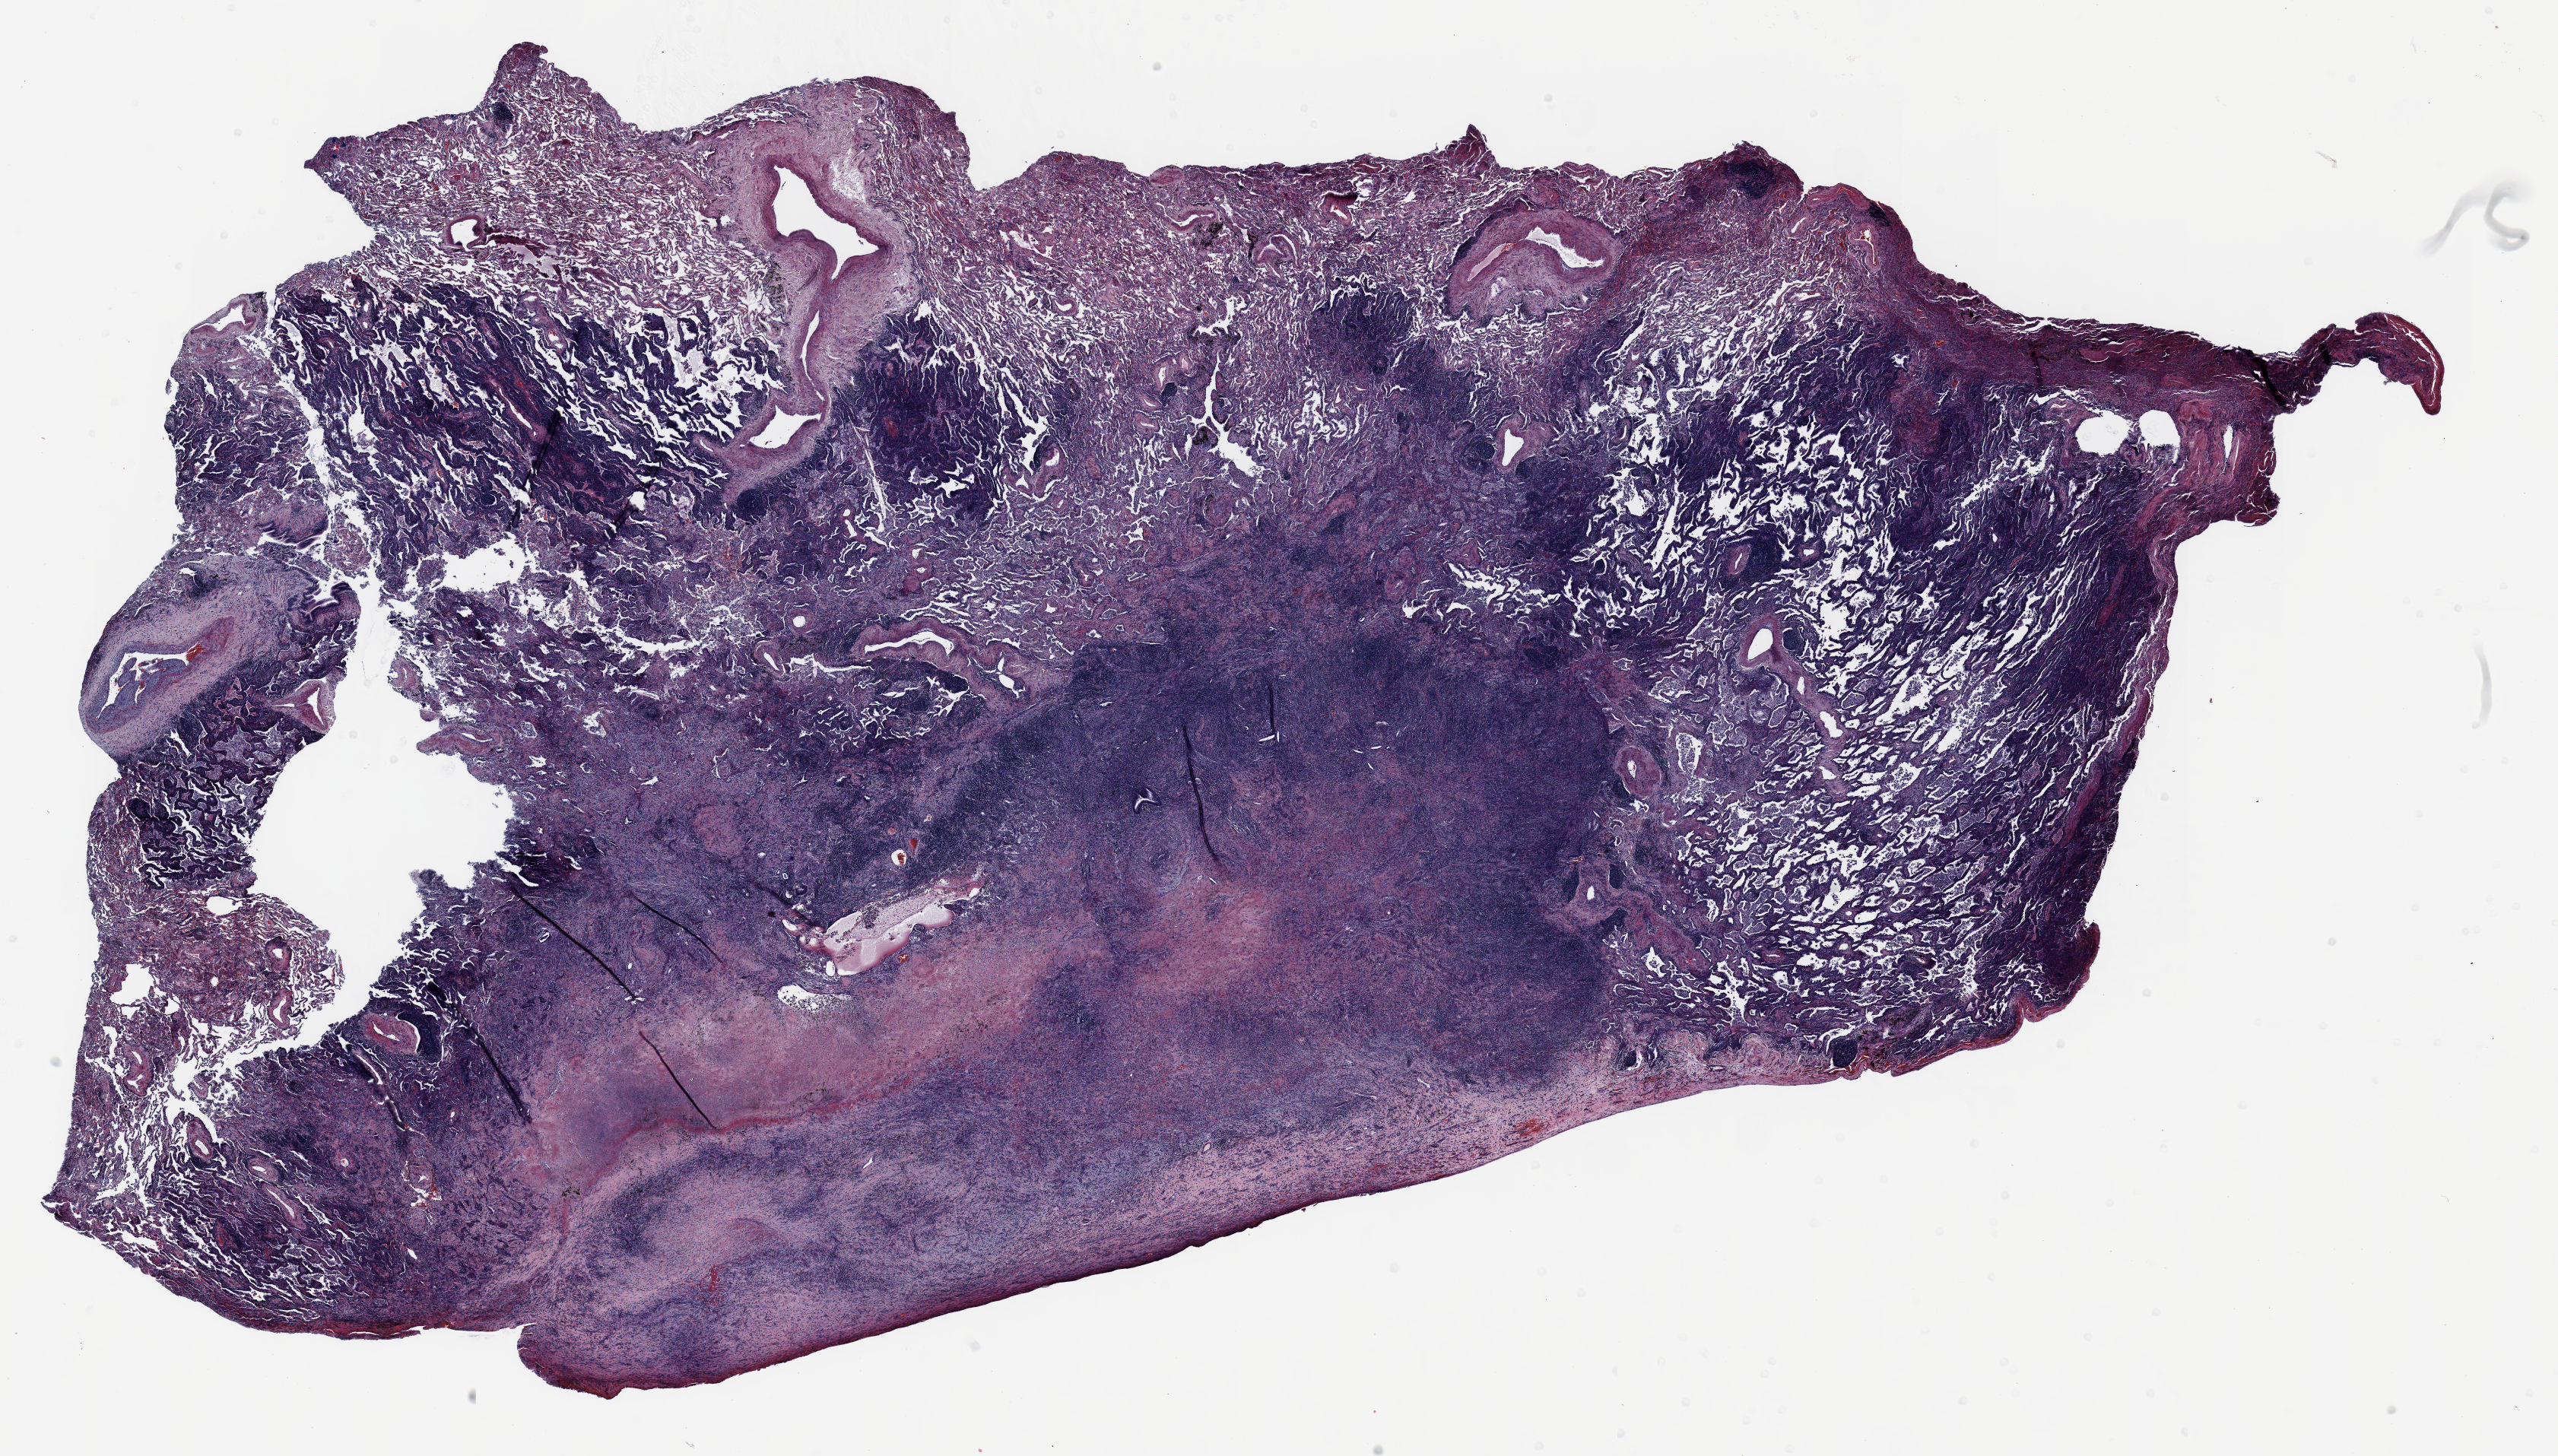
H&E whole-slide image, low-resolution overview of the scanned area, about 27.0 x 15.4 mm (acquisition: 20x scan); FFPE section; lung tissue. Male patient, aged 69 at enrolment. Former smoker at enrolment. Grade: well differentiated (G1).
Participant's lung-cancer diagnosis: Bronchiolo-alveolar adenocarcinoma, NOS. Stage (AJCC 6th edition): IB. Primary tumour location (clinical record): right lower lobe. Tumour size (pathology): 23 mm.